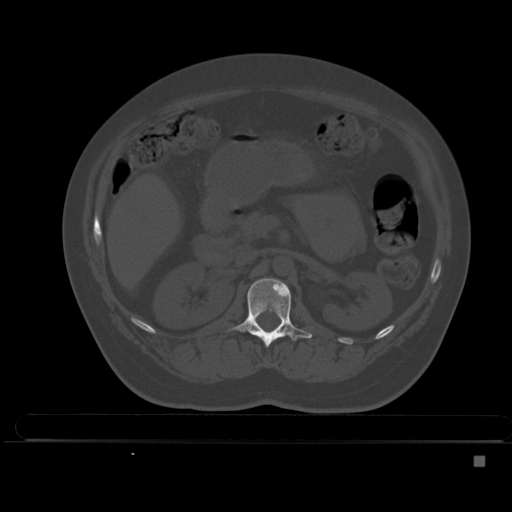
CT including the spine, one axial slice; position 194 of 495 along the scan axis; bone window (W 1800 / L 400 HU); 1.5 mm slice thickness; 512 × 512 image matrix, field of view 404 × 404 mm. Patient: female, 33 years. From the clinical record (not read from this slice): primary cancer: breast.
Annotated regions visible in this slice (semi-automatic segmentation, software-assisted and operator-edited):
- L1 vertebra: bounding box [x1, y1, x2, y2] px = [226, 278, 312, 347]